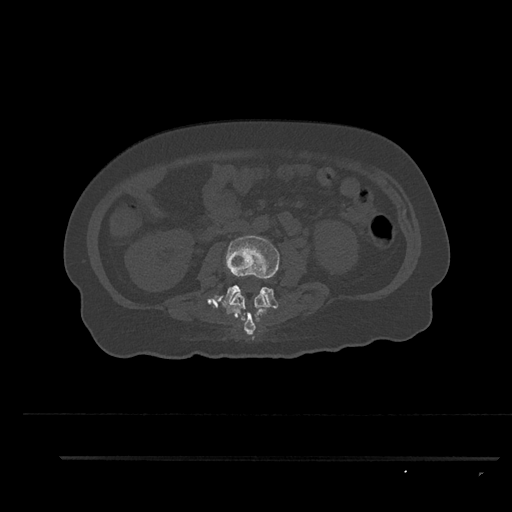
CT including the spine, one axial slice. Slice 116 of 797 in the series (ordered by position). Reconstruction kernel Br40s/3. Bone window (W 1800 / L 400 HU). 512 × 512 image matrix. Patient: female, 44 years. From the clinical record (not read from this slice): primary cancer: renal; vertebrae with lytic lesions (as recorded): L1.
Annotated regions visible in this slice (semi-automatic segmentation, software-assisted and operator-edited):
- L2 vertebra: bounding box <224,293,268,335> (left, top, right, bottom; pixels)
- L3 vertebra: <218,235,280,309>